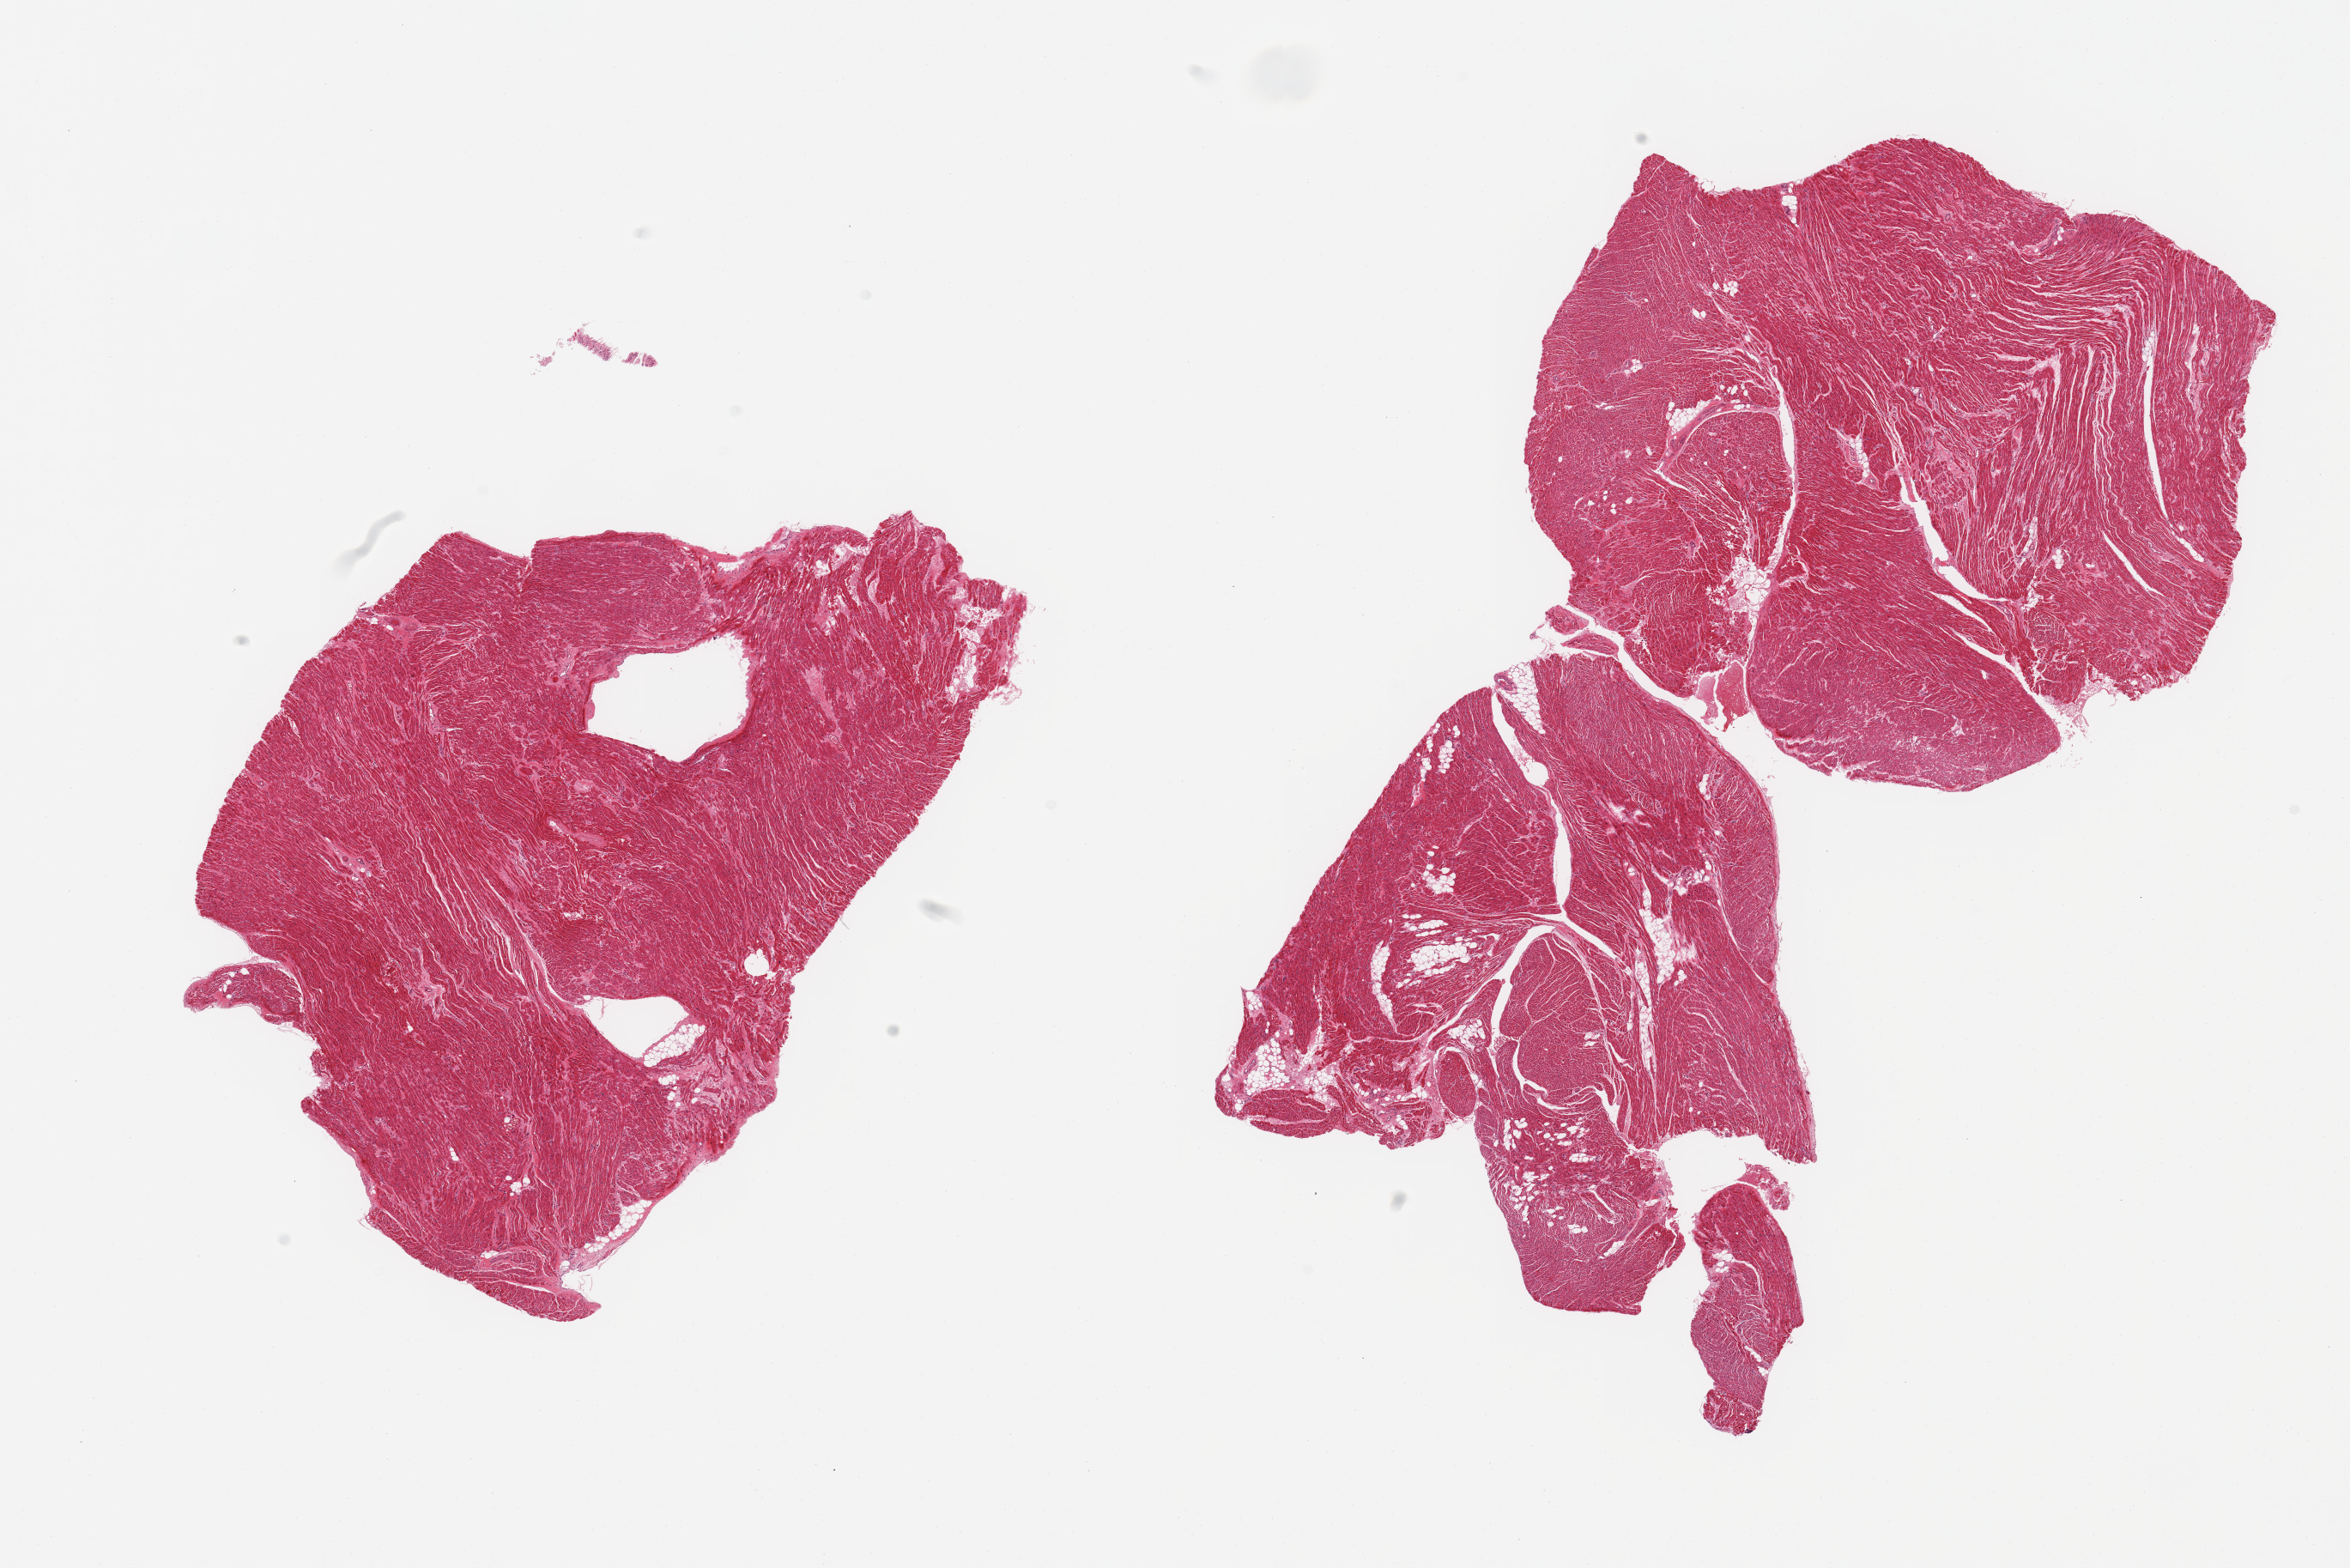
Digitized haematoxylin and eosin-stained section, brightfield, a low-resolution overview of the entire scanned area, about 21.7 x 14.5 mm, PAXgene-fixed, paraffin-embedded tissue, section of auricular appendage (target tissue), tissue donor sample. Female donor.
Reviewer comment on this tissue sample: 2 pieces; includes minimal fat.